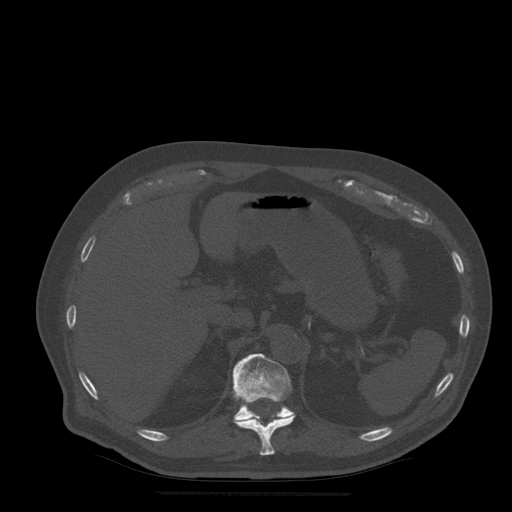
CT including the spine, one axial slice; slice 233 of 522 in the series (ordered by position); bone window (W 1800 / L 400 HU); 1.25 mm slice thickness; 512 × 512 image matrix, field of view 420 × 420 mm. Patient age 72 years. Case-level facts recorded for this patient, not image findings: primary cancer: prostate.
Structures marked on this image (semi-automatic segmentation, software-assisted and operator-edited):
- T11 vertebra: bounding box [x1, y1, x2, y2] px = [234, 413, 296, 456]
- T12 vertebra: [233, 354, 294, 420]